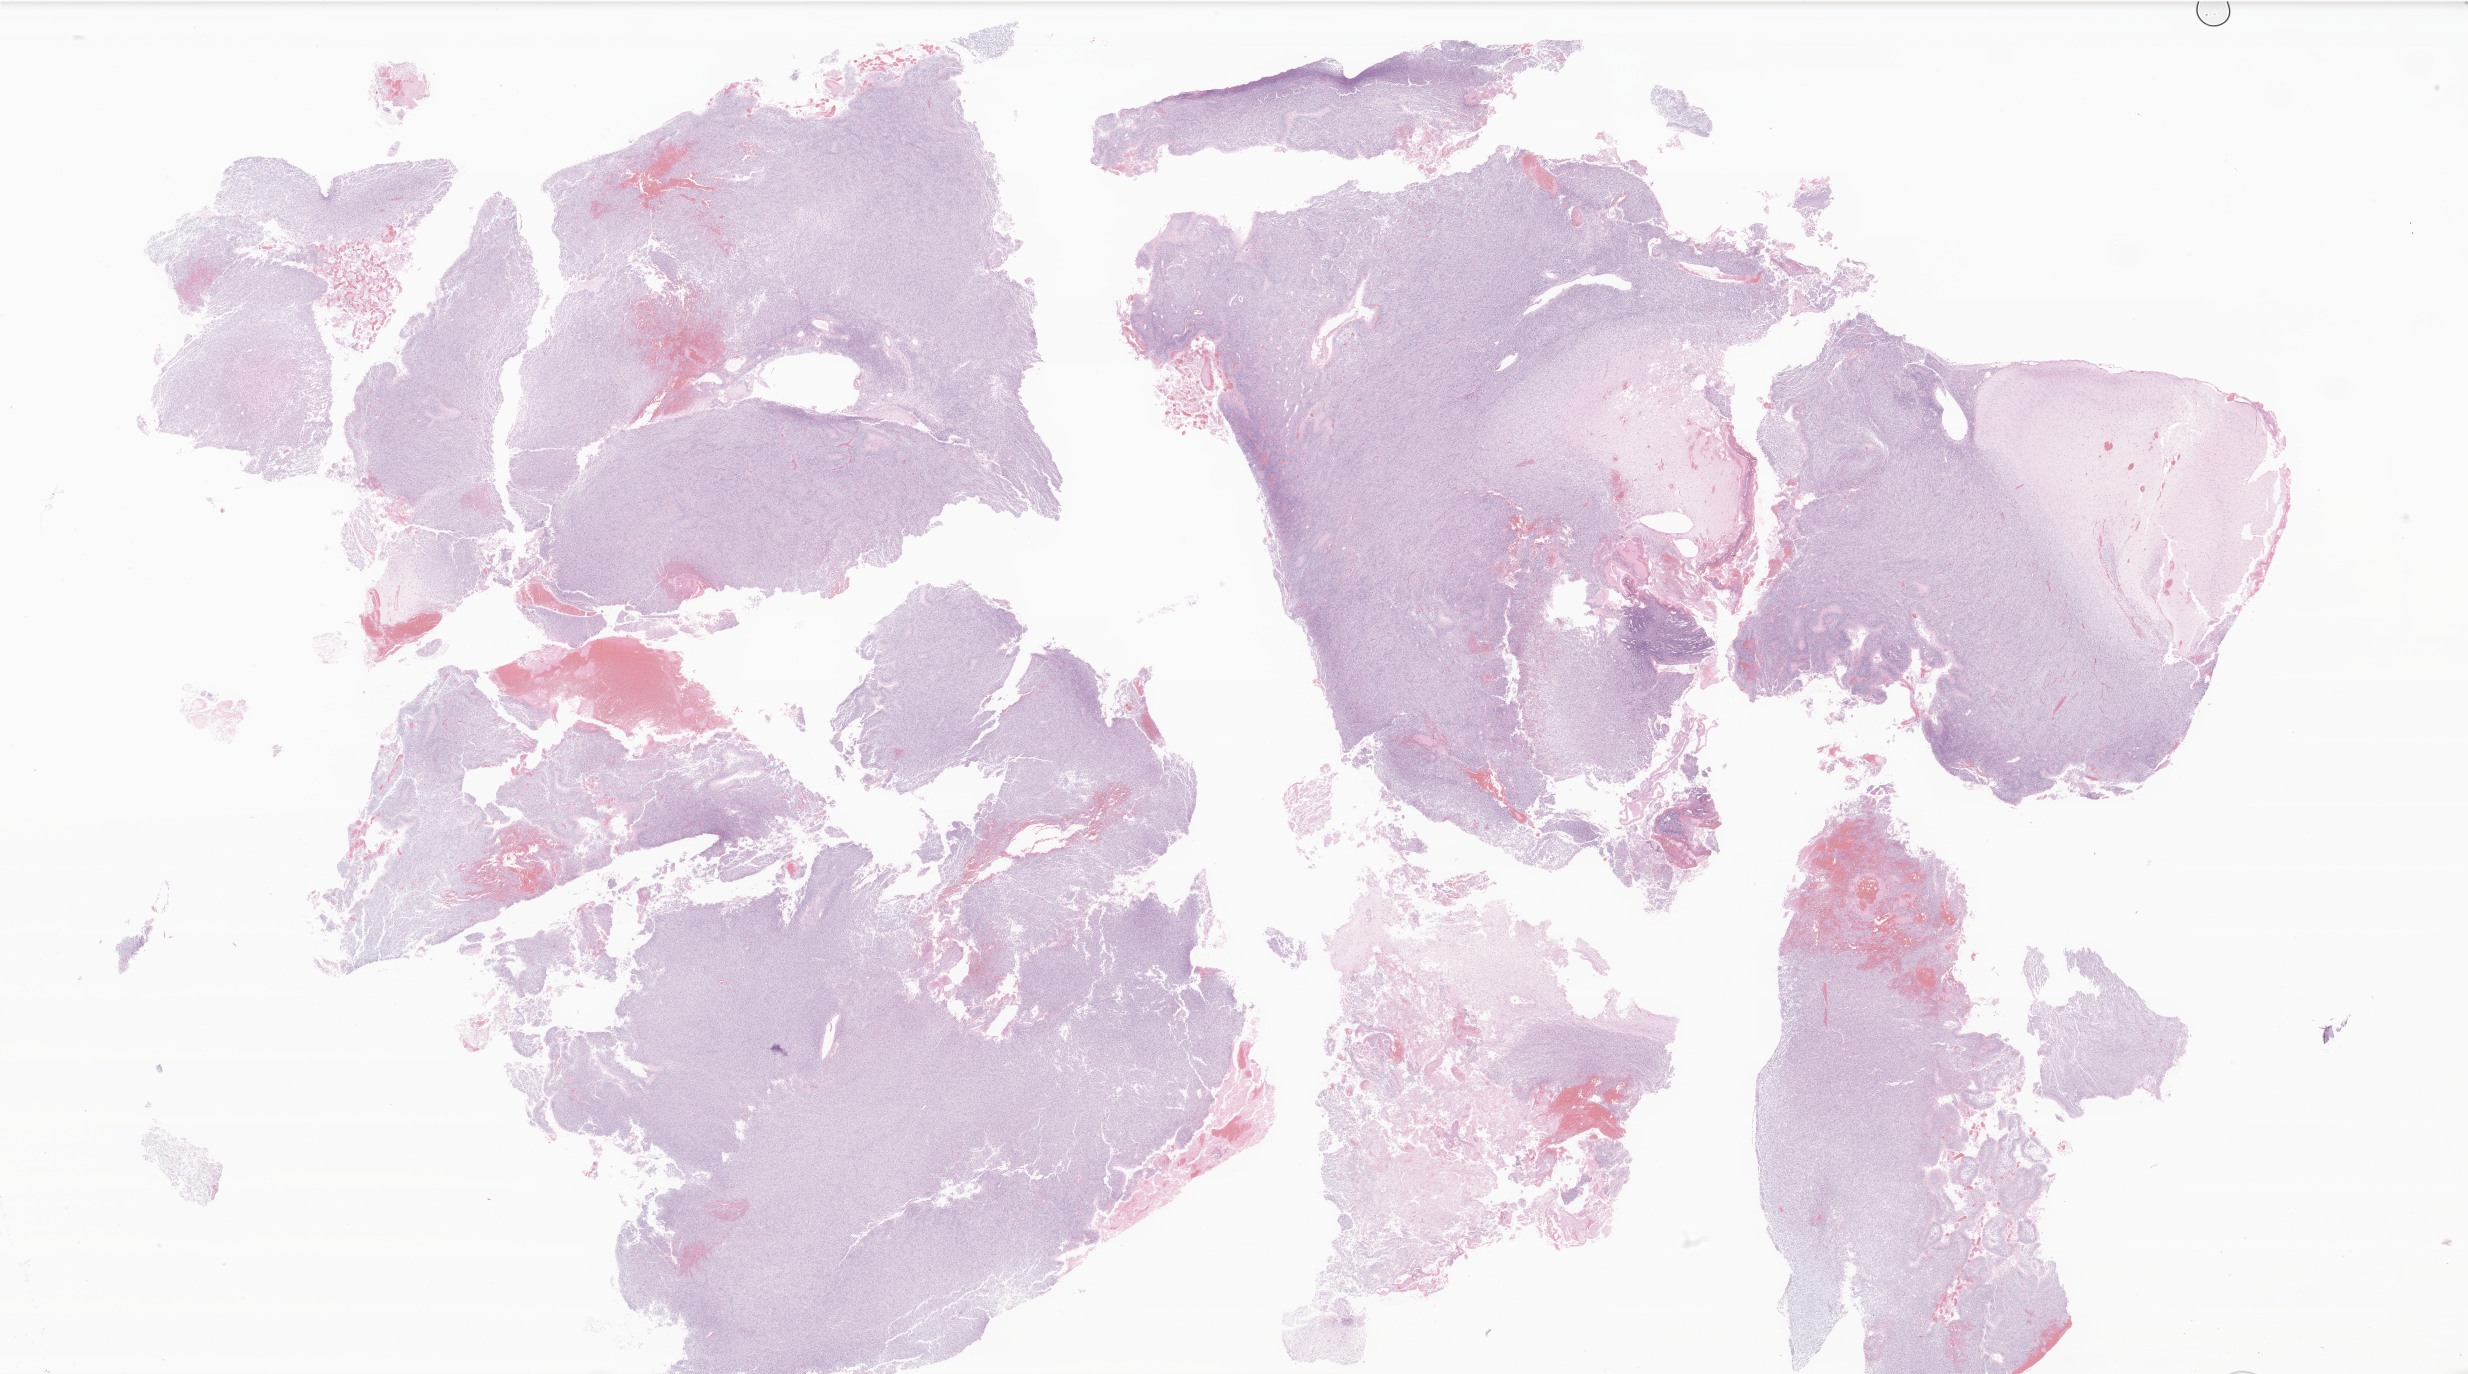
Whole-slide image, H&E stain of tumor tissue from the brain — low-resolution overview of the scanned area, about 41.6 x 23.2 mm. FFPE section. Female patient, age 101 days.
• recorded diagnosis: Glioma, malignant